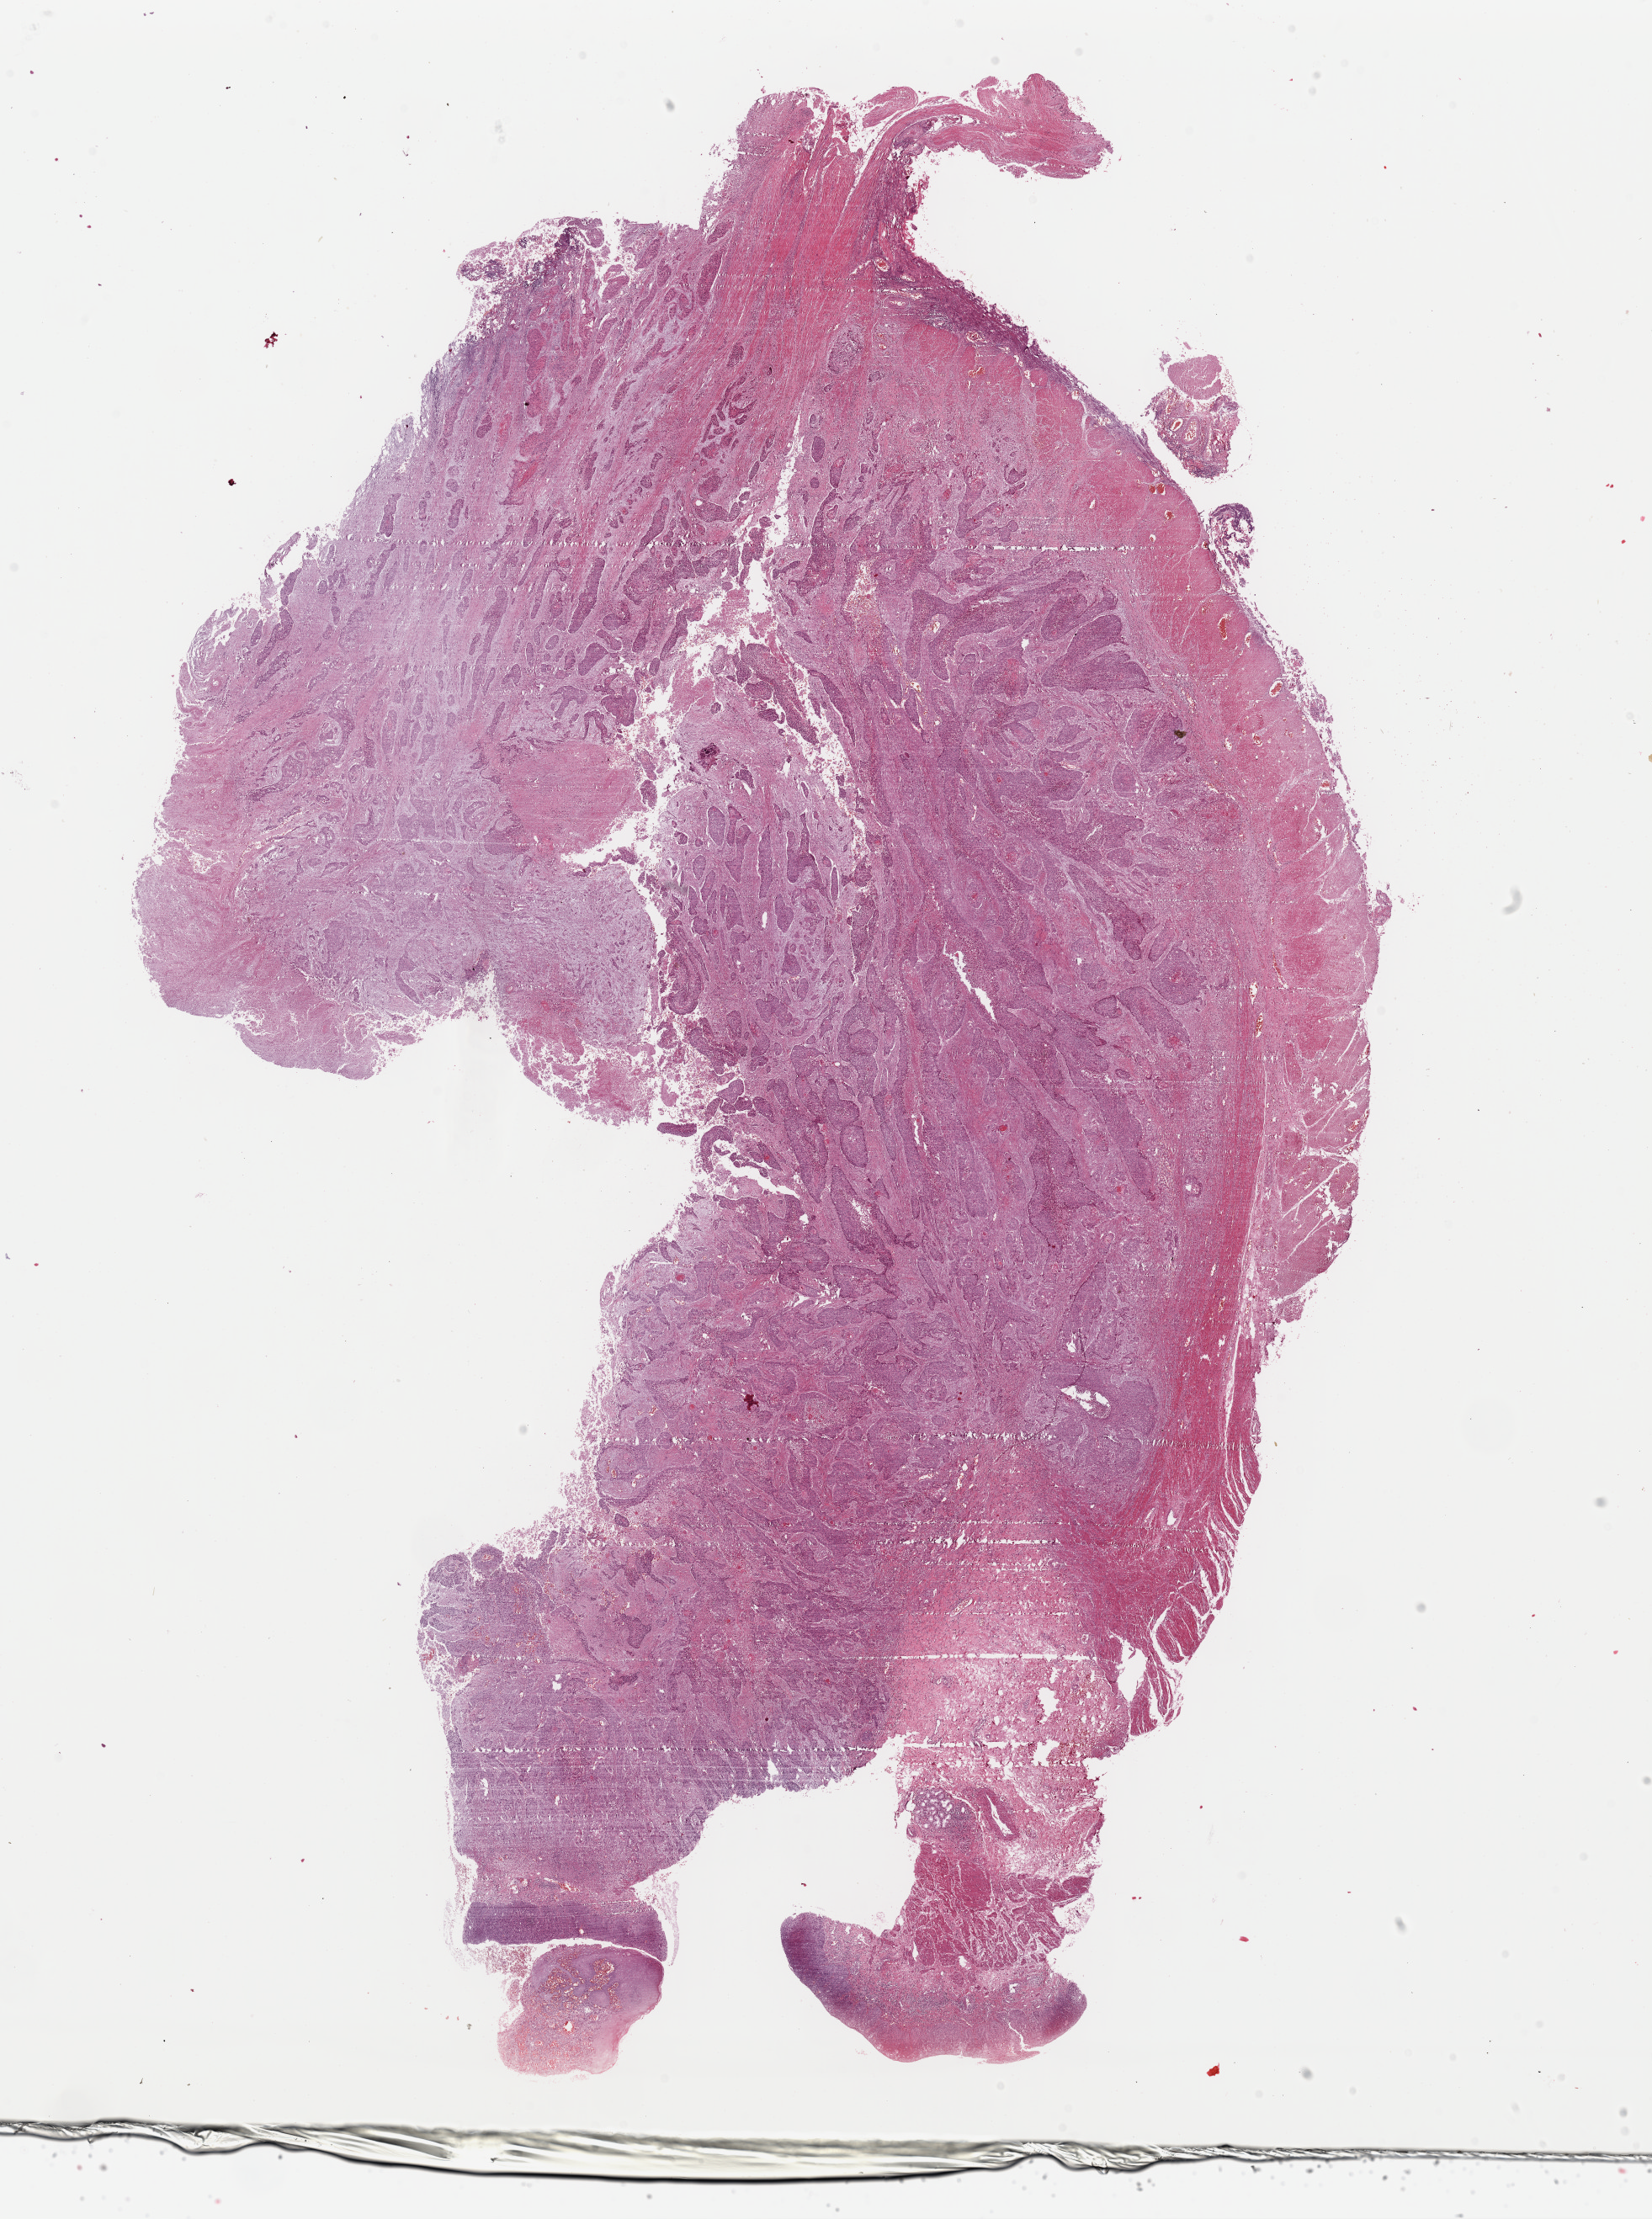
Digitized H&E-stained tissue section (whole slide) — whole scanned area (about 15.5 x 20.8 mm) shown as a low-resolution overview; FFPE section; esophagus, primary tumour sample. Patient: male, age at initial diagnosis 57 years. Histologic grade: G1 (well differentiated).
Diagnosis: Squamous cell carcinoma, NOS (middle third of esophagus). TNM: T3 N0 M0. AJCC pathologic stage: IIA.